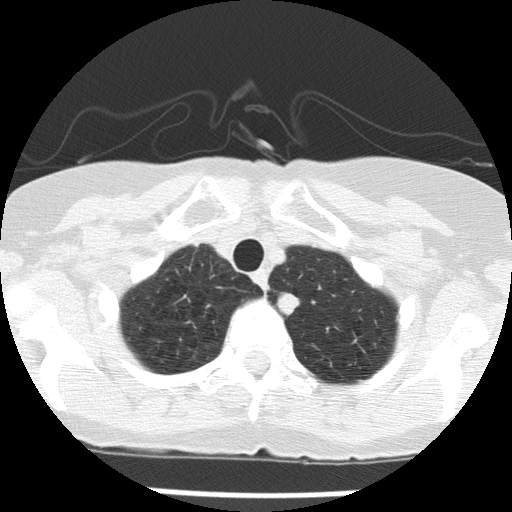
Low-dose screening chest CT, one axial slice. Position 126 of 143 along the scan axis. 120 kVp. Lung window (W 1500 / L -600 HU). 2 mm slice thickness. 512 × 512 image matrix.
Structures marked on this image (manually delineated by an expert):
- lesion 1 (tumor, upper lobe of left lung): bounding box (x1, y1, x2, y2) in pixels: (277, 293, 300, 316)